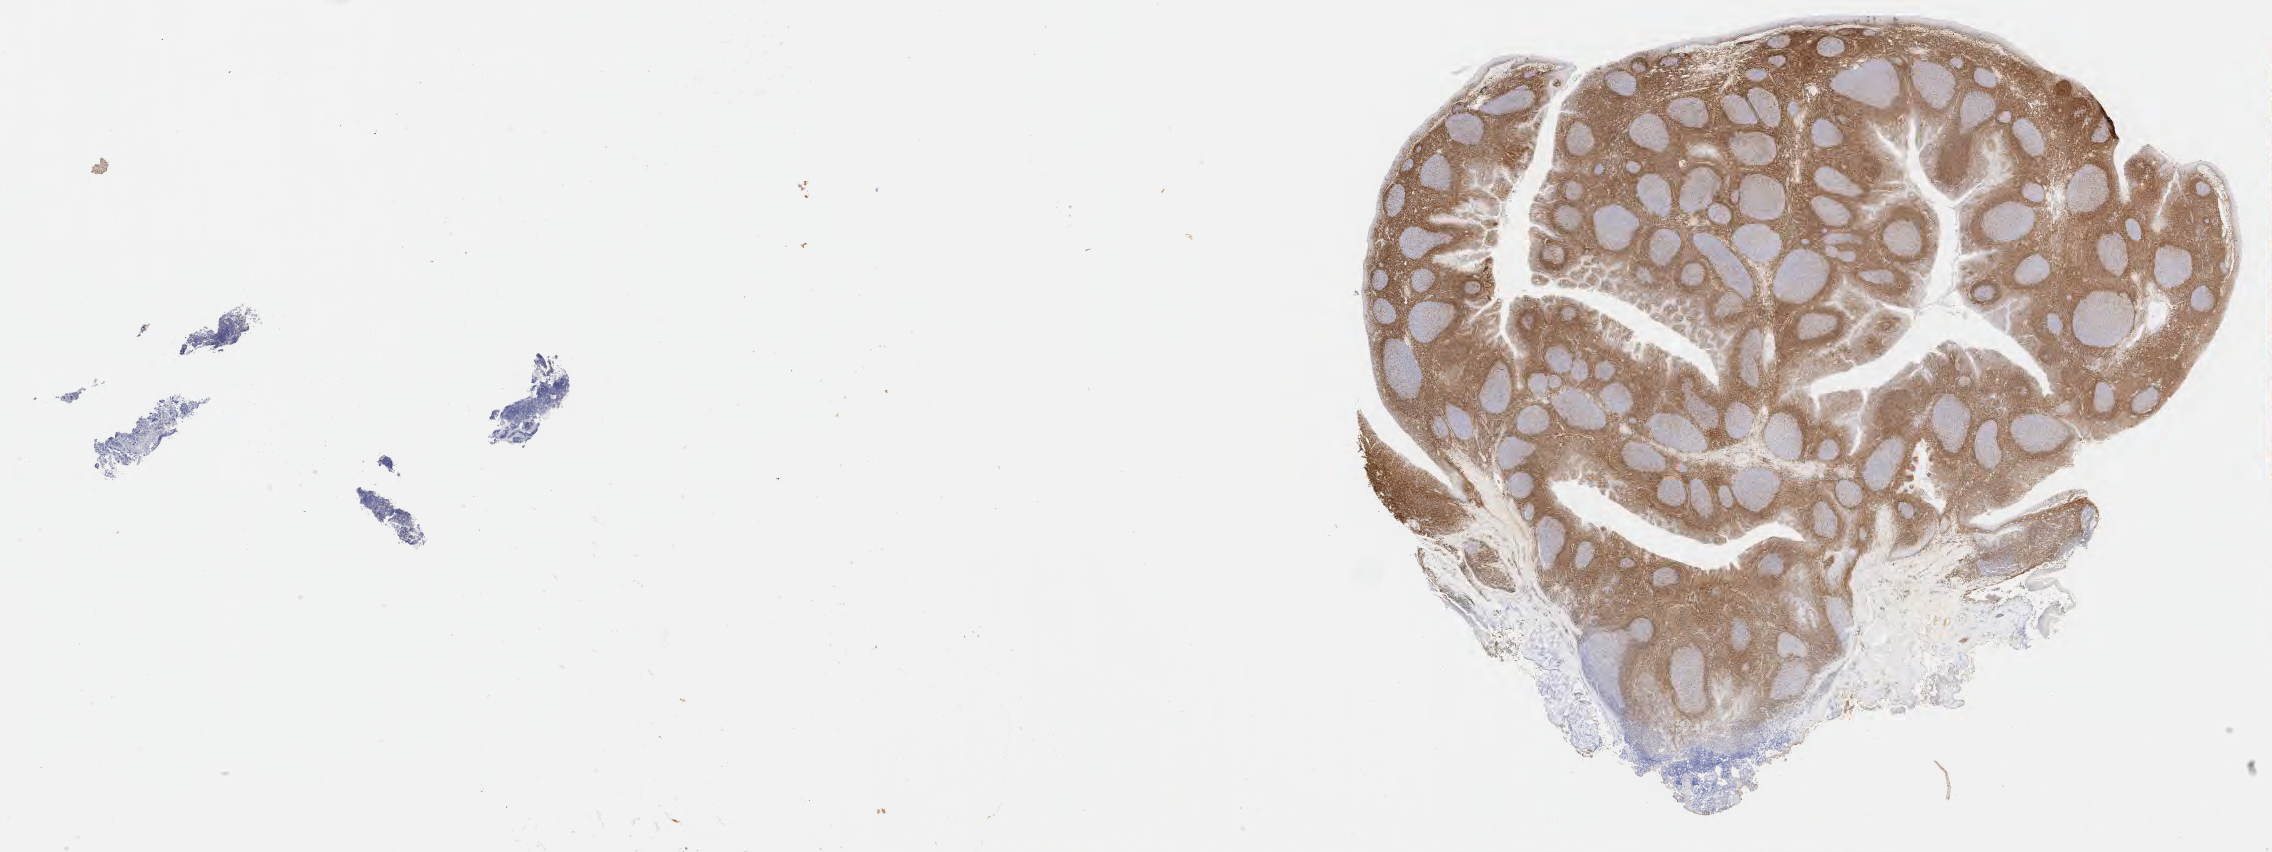
Whole-slide image, immunohistochemical stain for BCL2 — low-resolution overview of the scanned area, about 36.7 x 13.8 mm; tumor tissue; site: lymph node of head and neck. Female patient; age at initial diagnosis 4 years.
Diagnosis: Burkitt lymphoma, NOS.